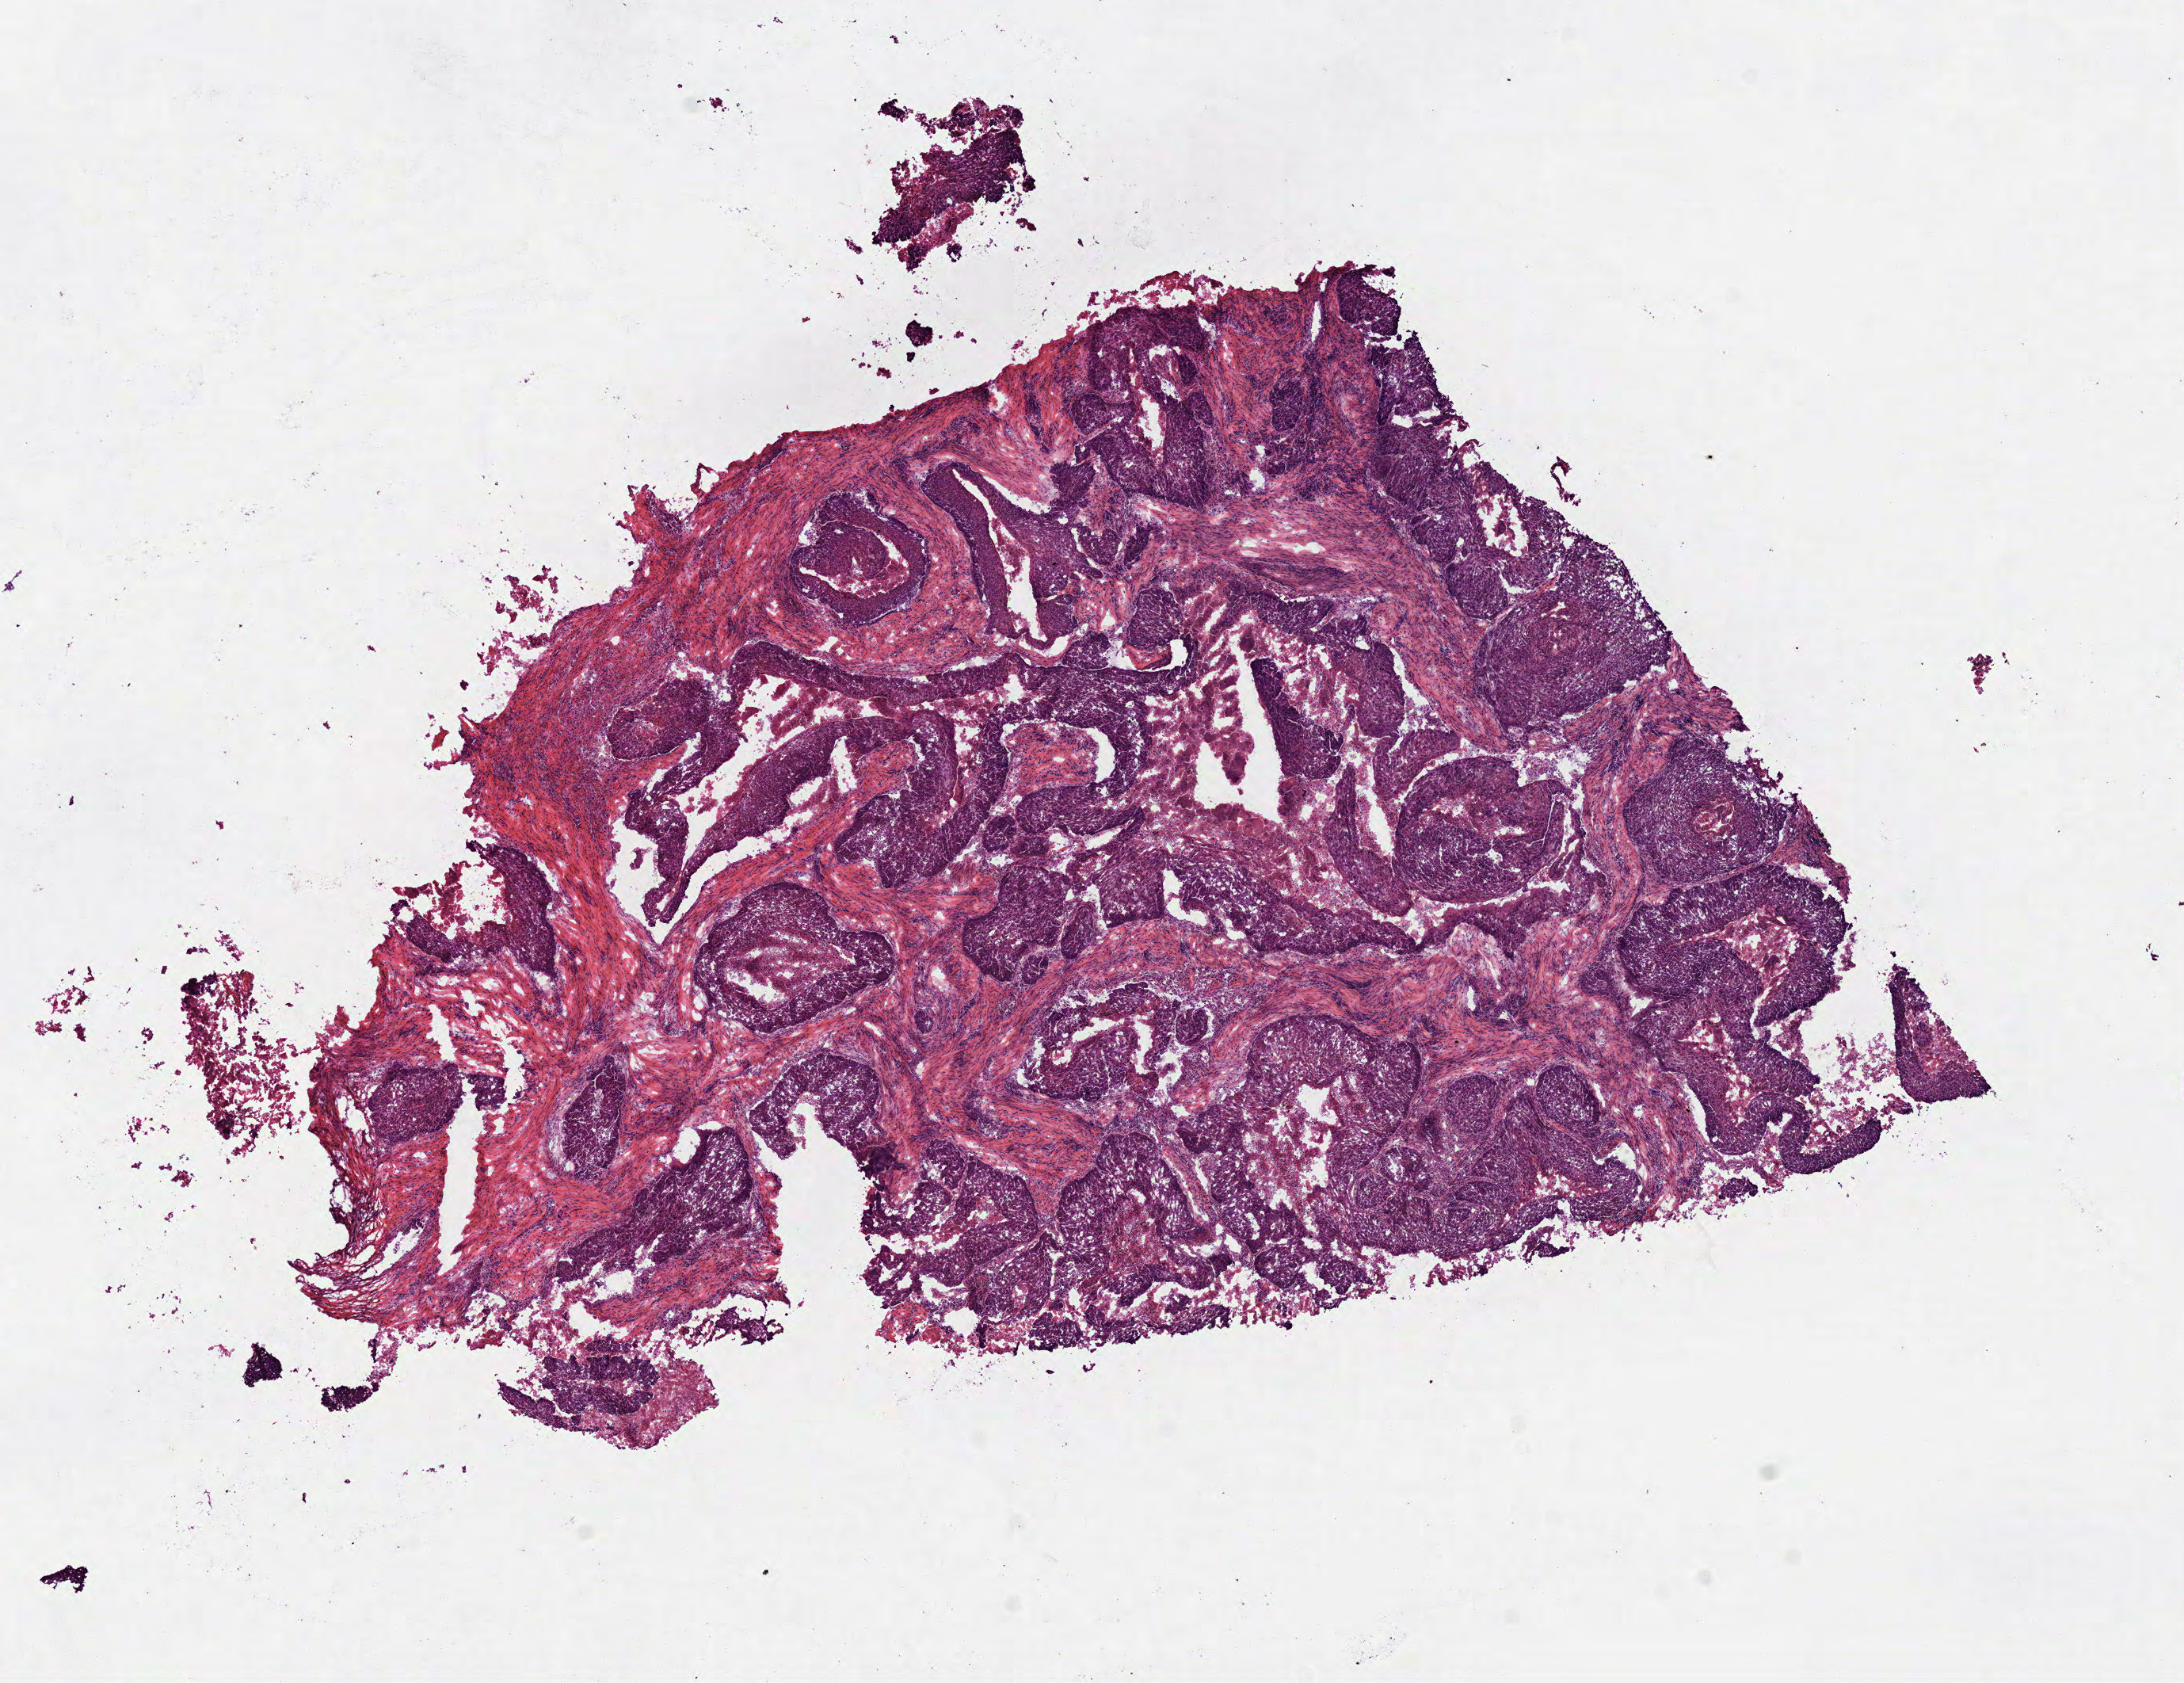
Whole-slide histology image, H&E-stained, low-resolution overview of the scanned area, about 11.1 x 8.6 mm (from a 40x scan), frozen section from the bottom of the tissue portion, sample: primary tumour, head and neck. Patient: male, age at initial diagnosis 68 years. Histologic grade: G2 (moderately differentiated). Slide review estimates, as recorded: tumour cells 90%, tumour nuclei 80%, normal cells 0%, stromal cells 0%, necrosis 10%. Infiltration values recorded for this section: lymphocyte infiltration 2%, monocyte infiltration 0%, neutrophil infiltration 5%.
* lymph nodes positive (case pathology): 5 of 10 examined
* AJCC pathologic stage: IVA (7th edition)
* histologic diagnosis: Squamous cell carcinoma, NOS (floor of mouth, NOS)